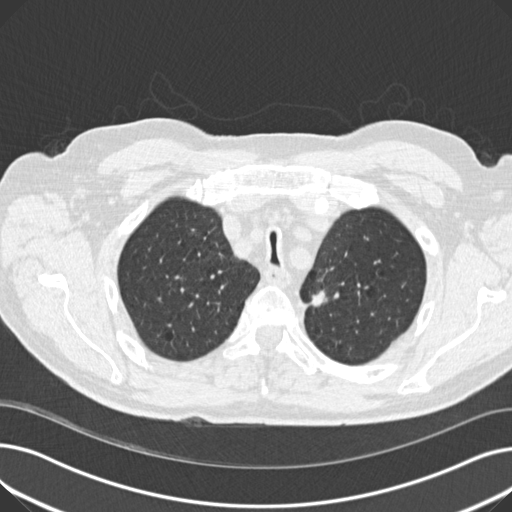
Low-dose screening chest CT, axial slice. Third annual screen. Lung window (W 1500 / L -600 HU). 2 mm slice thickness. Standard (soft-tissue) reconstruction kernel (B30f). Slice 43 of 191 in the series. Male participant, aged 70 years at enrolment. Current smoker at enrolment.
- Lesion marked by an expert reader, bounding box [x1, y1, x2, y2] px = [295, 274, 339, 315].
- The screening reader recorded 2 non-calcified nodules or masses ≥4 mm on this exam; which of them this box marks is not recorded.
- Official screen result: positive, other.